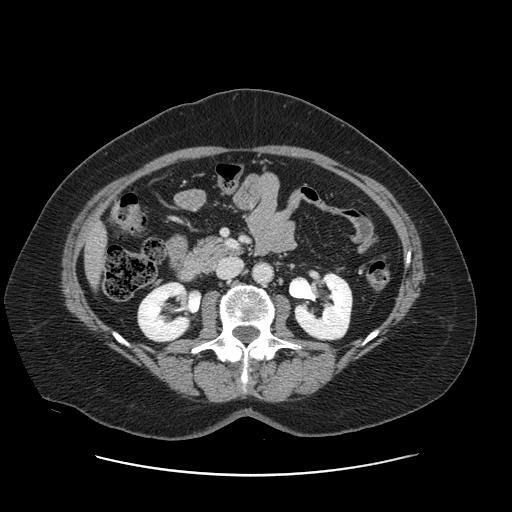
Contrast-enhanced abdominal CT, one axial slice. Slice 46 of 161 in the series (ordered by position). Intravenous contrast given. Soft-tissue window (W 400 / L 40 HU). 2.5 mm slice thickness. 512 × 512 image matrix, field of view 398 × 398 mm. Female patient, age 62 years. Case-level facts recorded for this patient, not image findings: diagnosis: colorectal cancer liver metastases, imaged before liver resection; multiple liver metastases: no; largest metastasis: 2.5 cm; disease in both lobes: no.
Structures marked on this image (expert manual segmentation):
- liver: bounding box (x1, y1, x2, y2) in pixels: (87, 228, 105, 282)